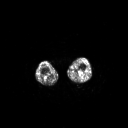
FDG PET of an extremity soft-tissue mass (from a PET/CT study), one axial slice. Slice 196 of 267 in the series (ordered by position). 128 × 128 image matrix, field of view 700 × 700 mm. Male patient, age 44 years. From the clinical record (not read from this slice): histological type: undifferentiated pleomorphic liposarcoma; grade: high; site of the primary tumour: left thigh.
Outlined on this slice (expert contour drawn on MRI and transferred to this co-registered scan by the dataset authors):
- gross tumour volume including surrounding oedema: box from (x=71, y=70) to (x=85, y=76) px